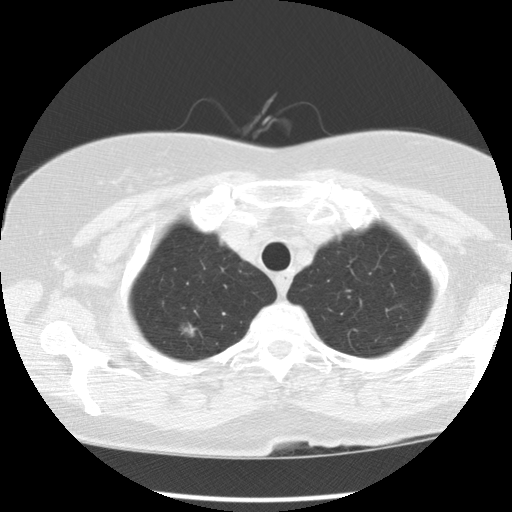
Chest CT (low-dose screening protocol), one axial image; third screening round (two years after baseline); lung window (W 1500 / L -600 HU); 2.5 mm slice thickness; slice 14 of 122 in the series; 512 × 512 image matrix. Female, age 72 years at enrolment. Former smoker at enrolment.
• Expert-annotated lung lesion, bounding box (x1, y1, x2, y2) in pixels: (166, 314, 207, 354).
• The screening reader recorded 4 non-calcified nodules or masses ≥4 mm on this exam; which of them this box marks is not recorded.